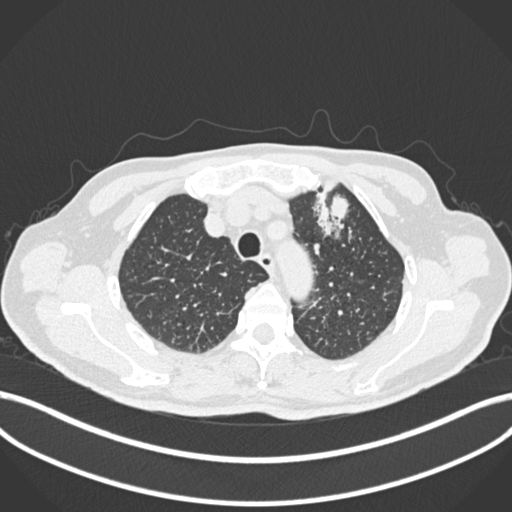
Chest CT, one axial slice; slice 207 of 261 in the series (ordered by position); reconstruction kernel B30f; 120 kVp; lung window (W 1500 / L -600 HU); 1 mm slice thickness; 512 × 512 image matrix. Patient: male, 74 years. From the clinical record (not read from this slice): clinical TNM (as recorded): T2b N0 M1c.
Outlined on this slice (rectangle marked by the reading radiologist):
- lung tumour (recorded histology: adenocarcinoma): box from (x=313, y=186) to (x=355, y=241) px